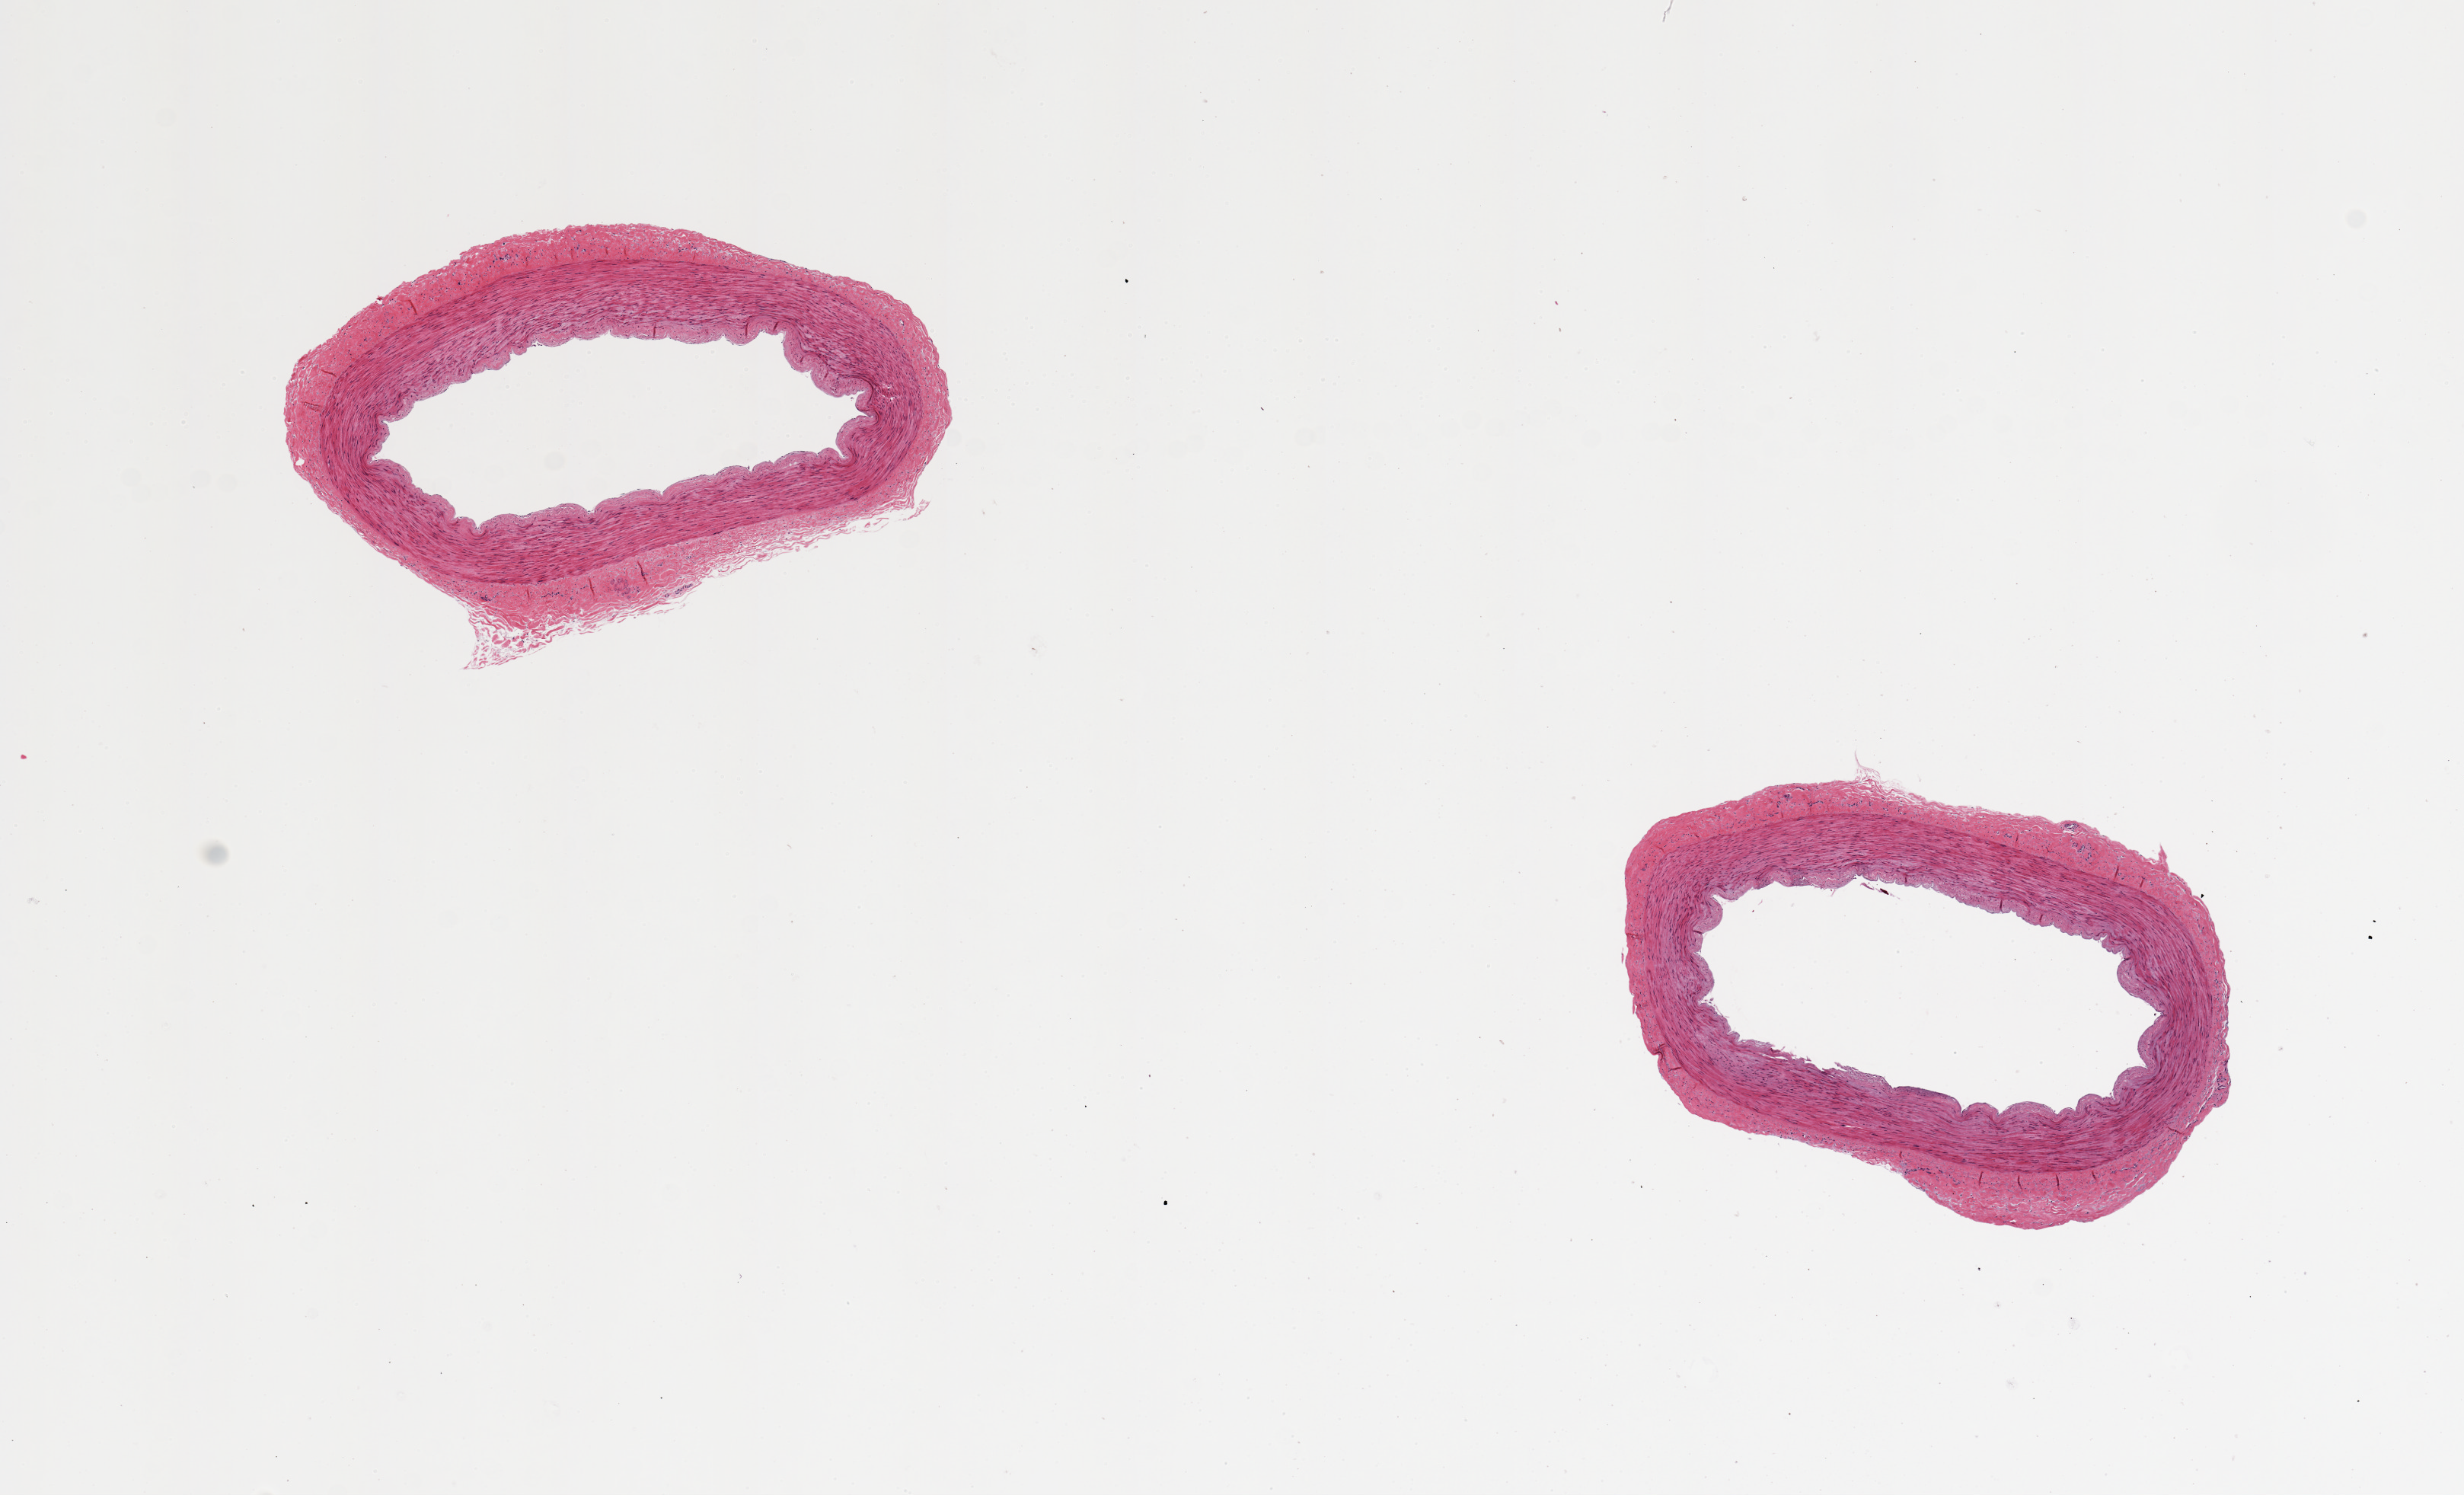
Digitized haematoxylin and eosin-stained section, shown as a low-resolution overview of the whole scanned area (about 12.8 x 7.8 mm, from a 20x scan), PAXgene-fixed paraffin-embedded (PFPE) section, target tissue: tibial artery, donor tissue sample. Donor: male.
Pathologist's review note for this sample: 2 pieces, well trimmed.